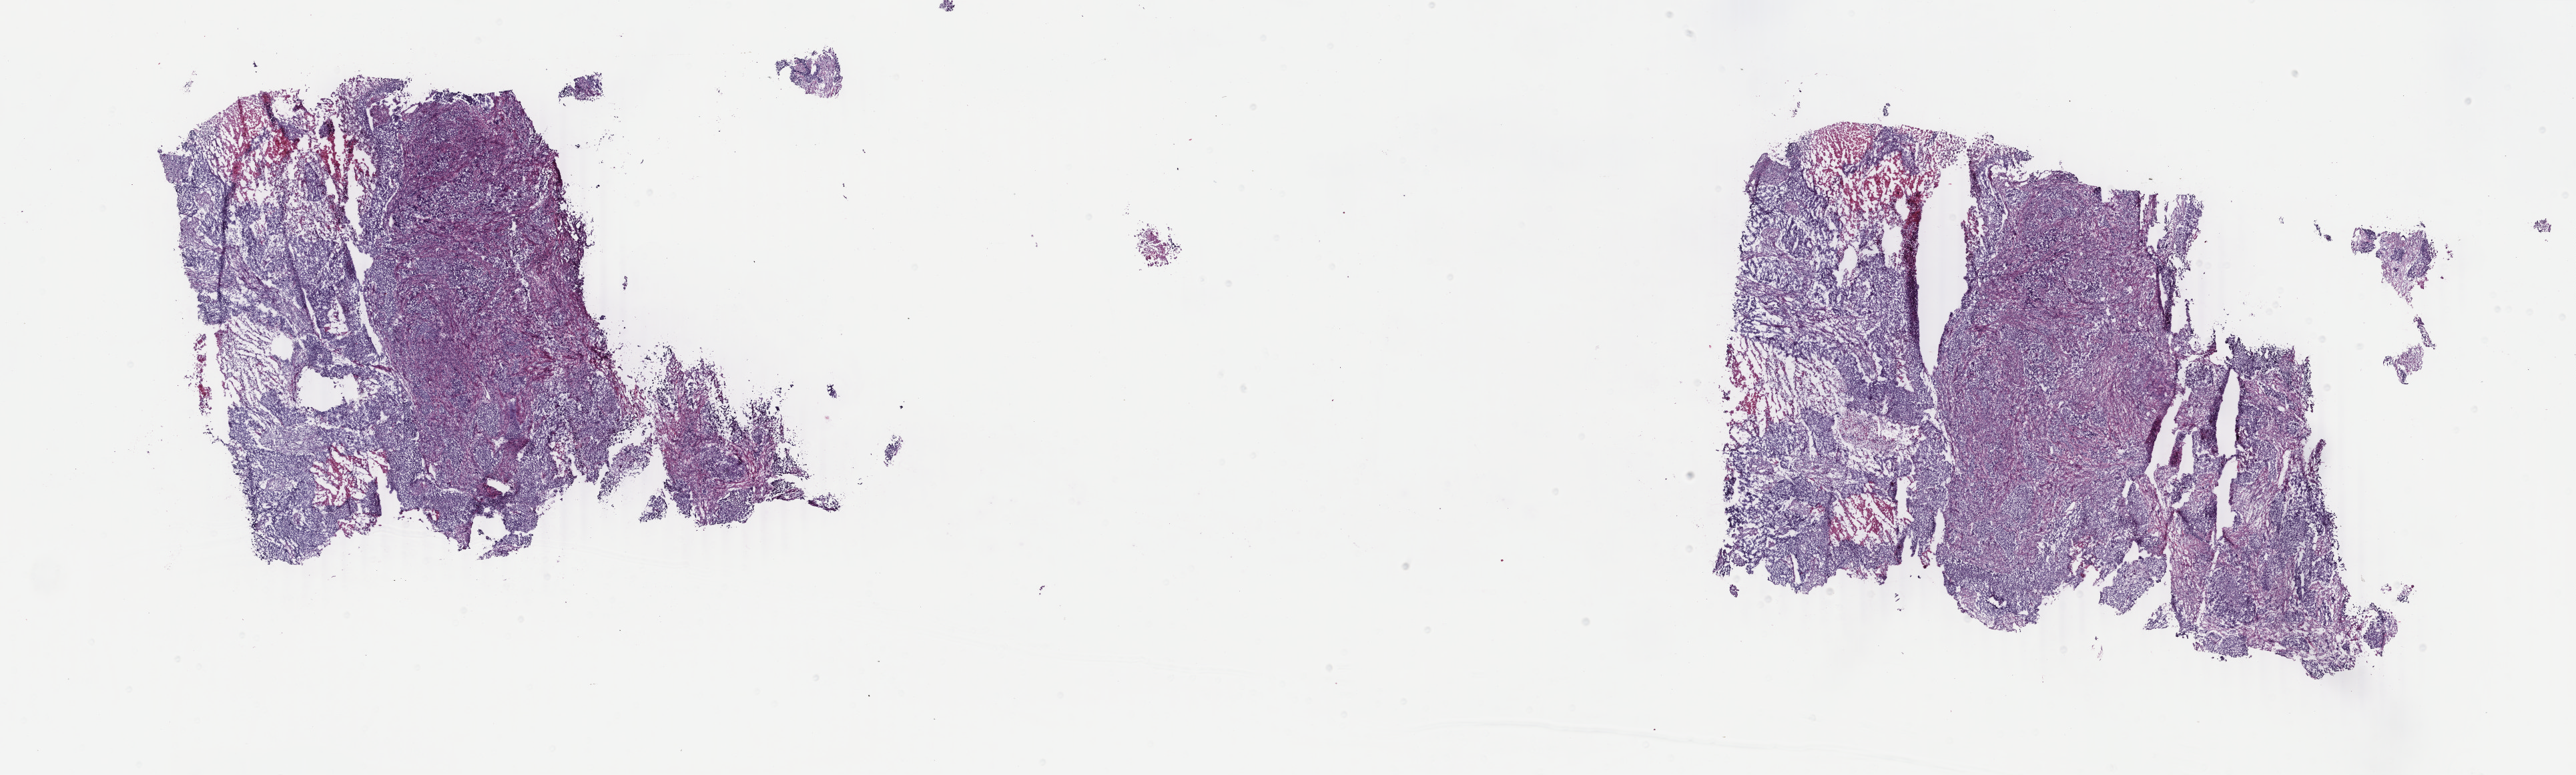
H&E-stained whole-slide image, shown as a low-resolution overview of the whole scanned area (about 30.7 x 9.2 mm, acquisition: 40x scan); frozen section from the bottom of the tissue portion; primary tumour sample from the uterus. Patient: female, age at initial diagnosis 50 years. Histologic grade: G3 (poorly differentiated). Composition of this section per pathologist review: tumour cells 70%, tumour nuclei 80%, normal cells 20%, stromal cells 0%, necrosis 10%. Infiltration values recorded for this section: lymphocyte infiltration 20%, monocyte infiltration 0%, neutrophil infiltration 10%.
• FIGO stage: IIIC1
• diagnosis: Carcinoma, undifferentiated, NOS (endometrium)